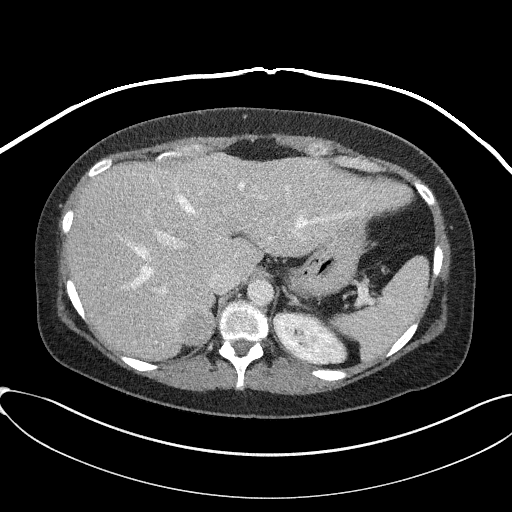
Contrast-enhanced abdominal CT, one axial slice; slice 64 of 95 in the series (ordered by position); 100 kVp; intravenous contrast given; soft-tissue window (W 400 / L 40 HU); 3 mm slice thickness; 512 × 512 image matrix. Female patient, age 46 years. From the clinical record (not read from this slice): diagnosis: adrenocortical carcinoma; tumour side: right adrenal; tumour size at pathology: 7.2 cm; Ki-67 index: 50 %; stage (as recorded): 4.
Annotated regions visible in this slice (semi-automatic segmentation, software-assisted and operator-edited):
- mass: bounding box [x1, y1, x2, y2] px = [177, 305, 214, 344]